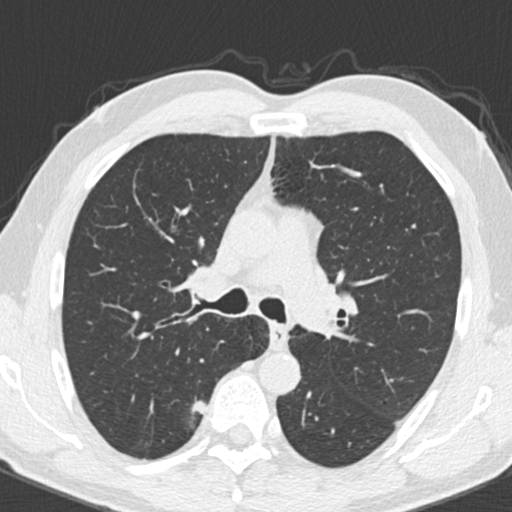
Low-dose screening chest CT, one axial slice; slice 128 of 192 in the series (ordered by position); reconstruction kernel B30f; 120 kVp; lung window (W 1500 / L -600 HU); 2 mm slice thickness; 512 × 512 image matrix, field of view 307 × 307 mm.
Outlined on this slice (expert manual segmentation):
- lesion 1 (tumor, upper lobe of right lung): bounding box (x1, y1, x2, y2) in pixels: (192, 399, 207, 415)